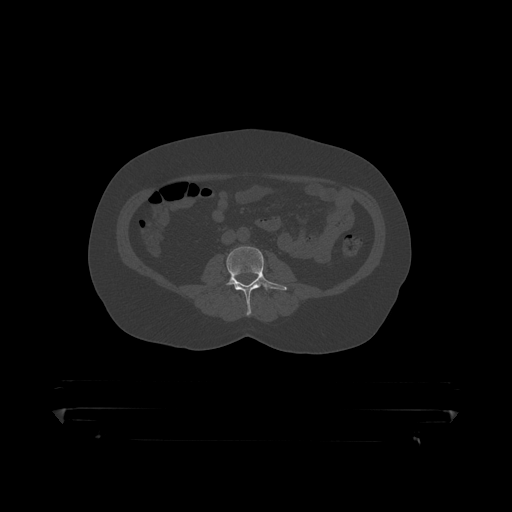
CT including the spine, one axial slice. Position 89 of 390 along the scan axis. 120 kVp. Bone window (W 1800 / L 400 HU). 1.25 mm slice thickness. 512 × 512 image matrix, field of view 650 × 650 mm. Male patient, age 60 years. Case-level facts recorded for this patient, not image findings: primary cancer: prostate.
Structures marked on this image (semi-automatically segmented with operator editing):
- L3 vertebra: bounding box <224,247,288,316> (left, top, right, bottom; pixels)